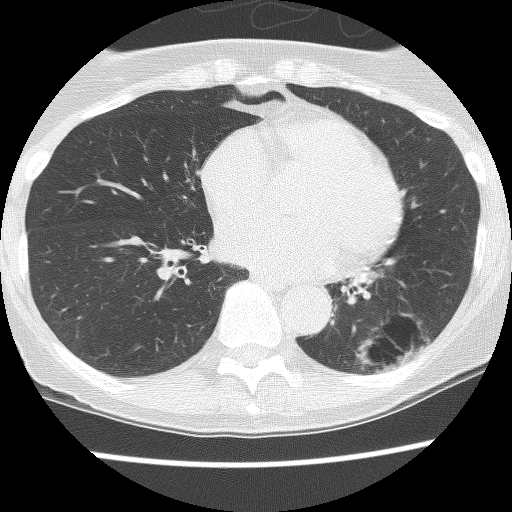
Axial slice from a low-dose chest CT screening exam; third screening round (two years after baseline); lung window (W 1500 / L -600 HU); 2.5 mm slice thickness; lung (sharp) reconstruction kernel (BONE); slice 79 of 130 in the series; 512 × 512 image matrix, field of view 290 × 290 mm. Female, age 61 years at enrolment.
Expert-annotated lung lesion, bounding box [x1, y1, x2, y2] px = [329, 289, 451, 391]. The screening reader recorded 2 non-calcified nodules or masses ≥4 mm on this exam (left lower lobe, left lower lobe); which of them this box marks is not recorded. Official screen result: positive, no significant change: stable abnormalities potentially related to lung cancer, unchanged since the prior screening exam. Lung cancer was diagnosed 166 days after this screen: non-small cell carcinoma, left lower lobe, poorly differentiated (G3), stage IB (AJCC 6th edition), 100 mm at pathology.